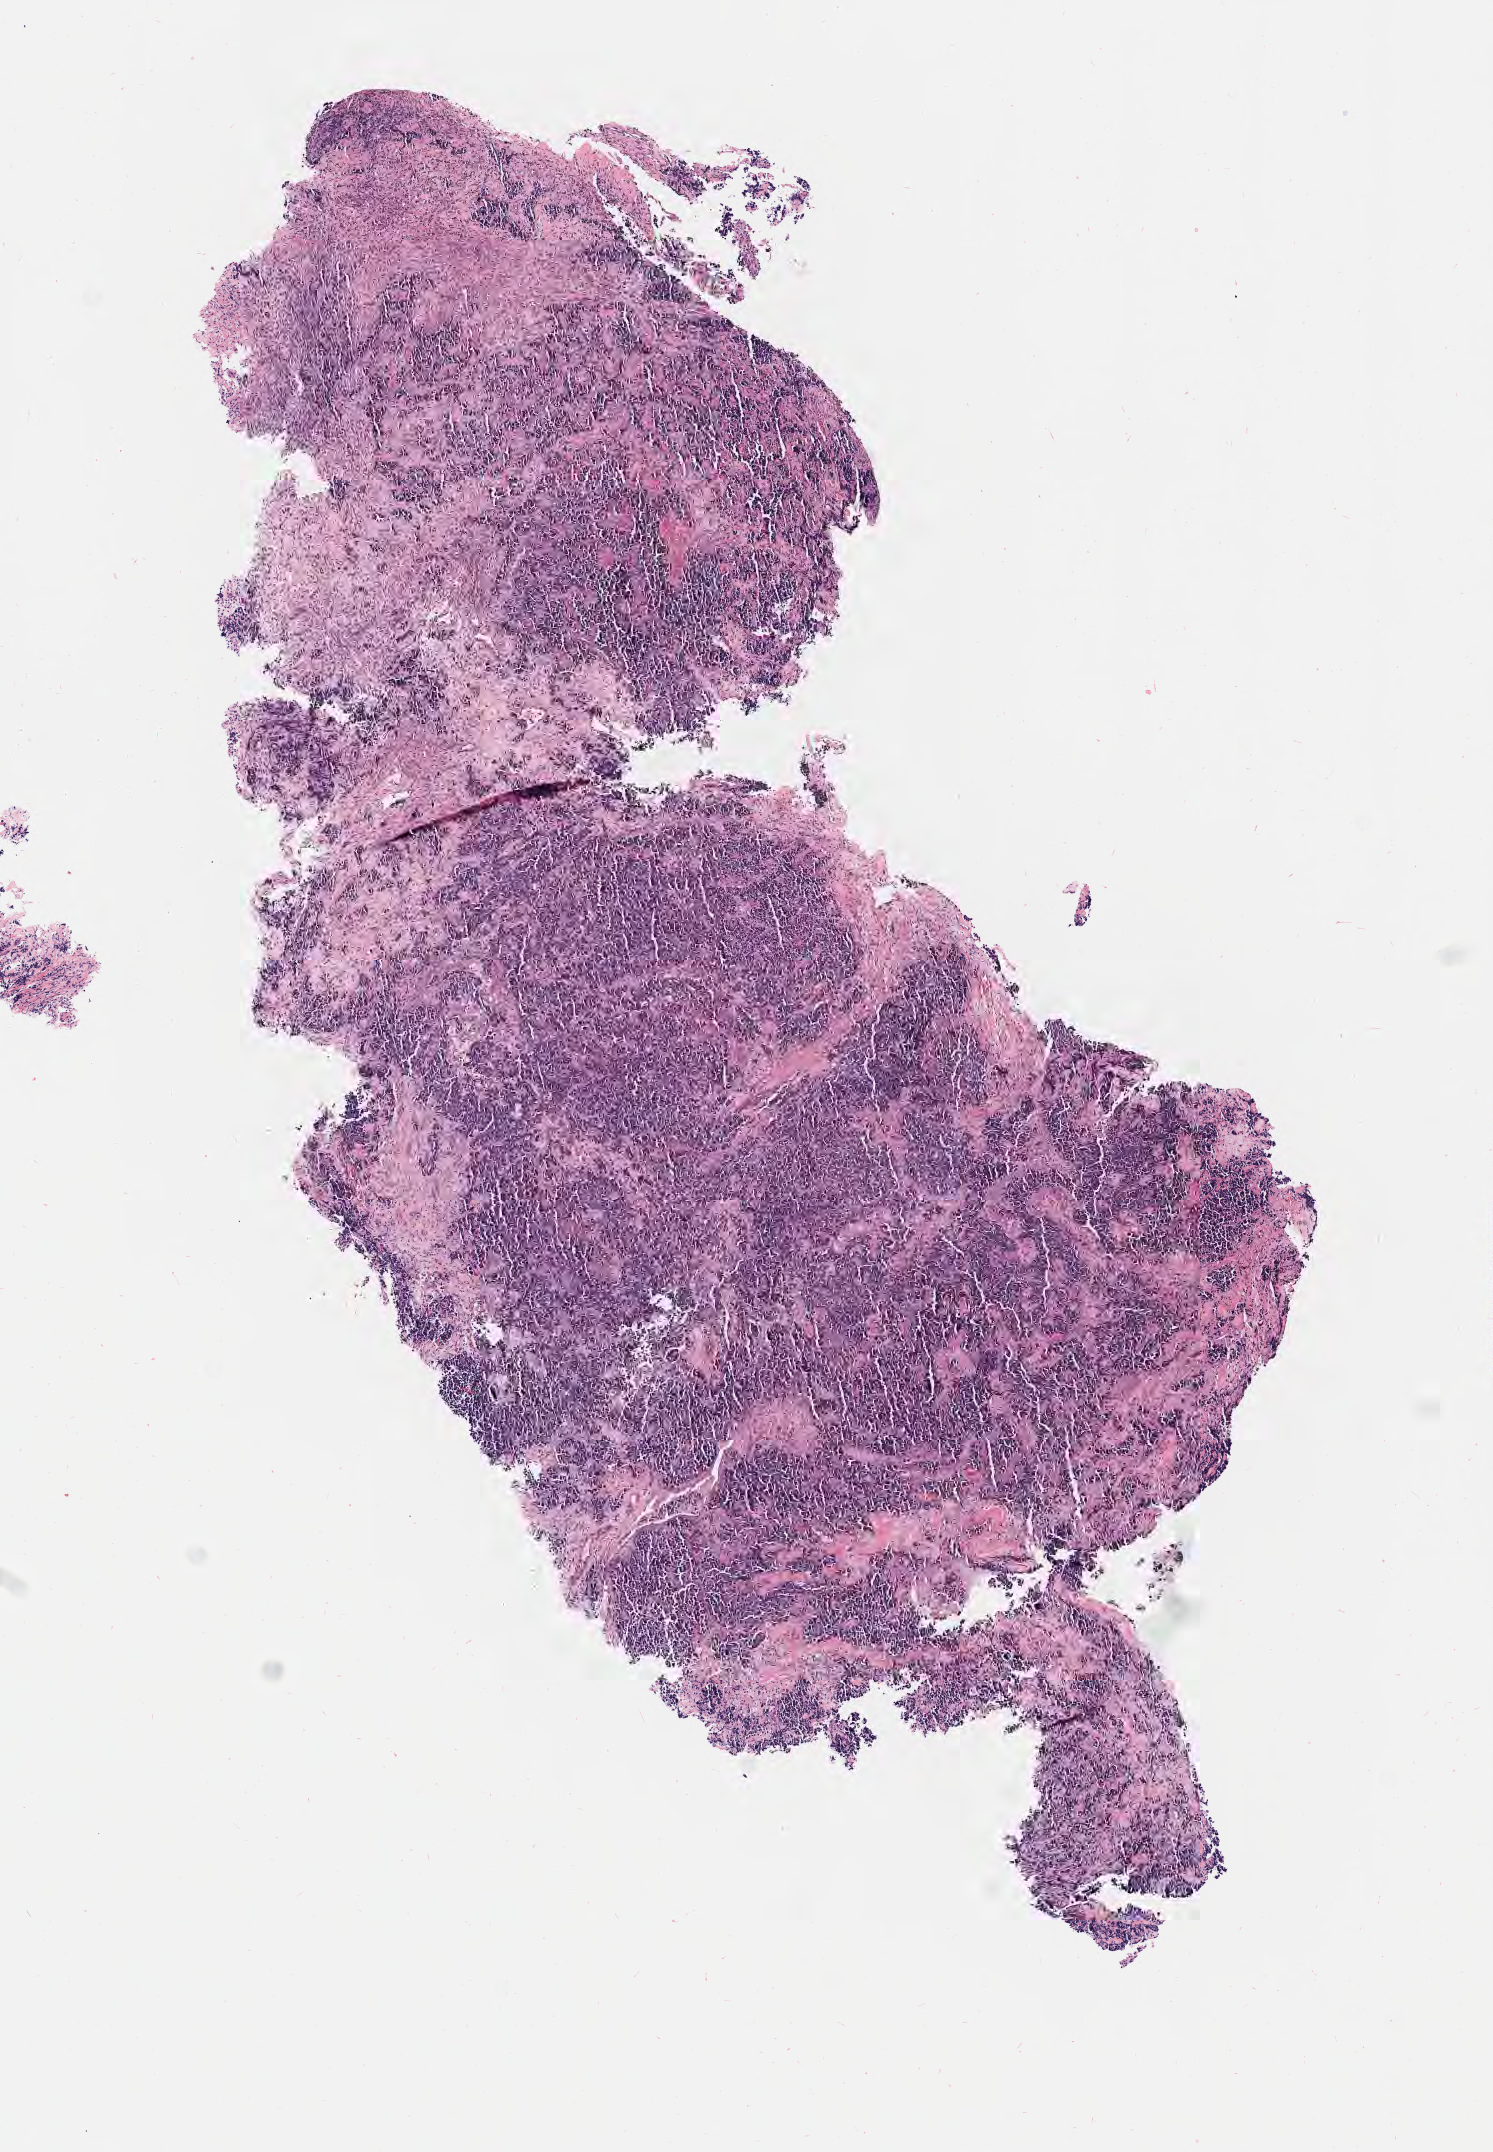
Whole-slide image, H&E stain, low-resolution overview of the scanned area, about 6.0 x 8.7 mm. Specimen: tumor tissue. Anatomic site: cervix. Patient: female, aged 43.
* histologic diagnosis: Lymphoepithelial carcinoma